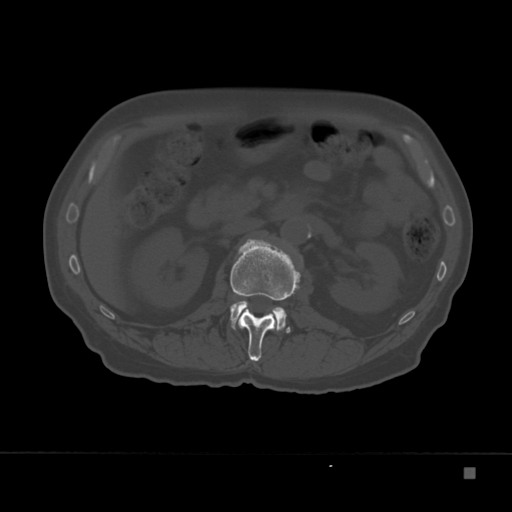
CT including the spine, one axial slice. Position 104 of 332 along the scan axis. Reconstruction kernel Br40s. Bone window (W 1800 / L 400 HU). 512 × 512 image matrix. Male patient, age 72 years. Case-level facts recorded for this patient, not image findings: primary cancer: skeletal.
Outlined on this slice (semi-automatic segmentation, software-assisted and operator-edited):
- L1 vertebra: bounding box <230,238,301,362> (left, top, right, bottom; pixels)
- L2 vertebra: <230,301,291,333>